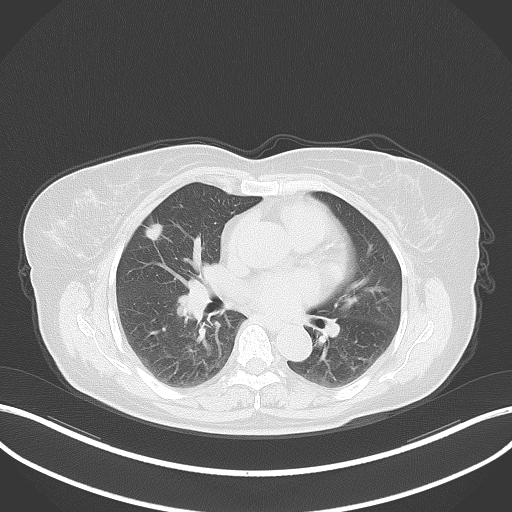
Chest CT, one axial slice; slice 35 of 64 in the series (ordered by position); lung window (W 1500 / L -600 HU); 512 × 512 image matrix. Female patient, age 55 years. Case-level facts recorded for this patient, not image findings: clinical TNM (as recorded): T1b N0 M0.
Annotated regions visible in this slice (bounding box drawn by a radiologist):
- lung tumour (recorded histology: adenocarcinoma): bounding box (x1, y1, x2, y2) in pixels: (143, 221, 166, 241)